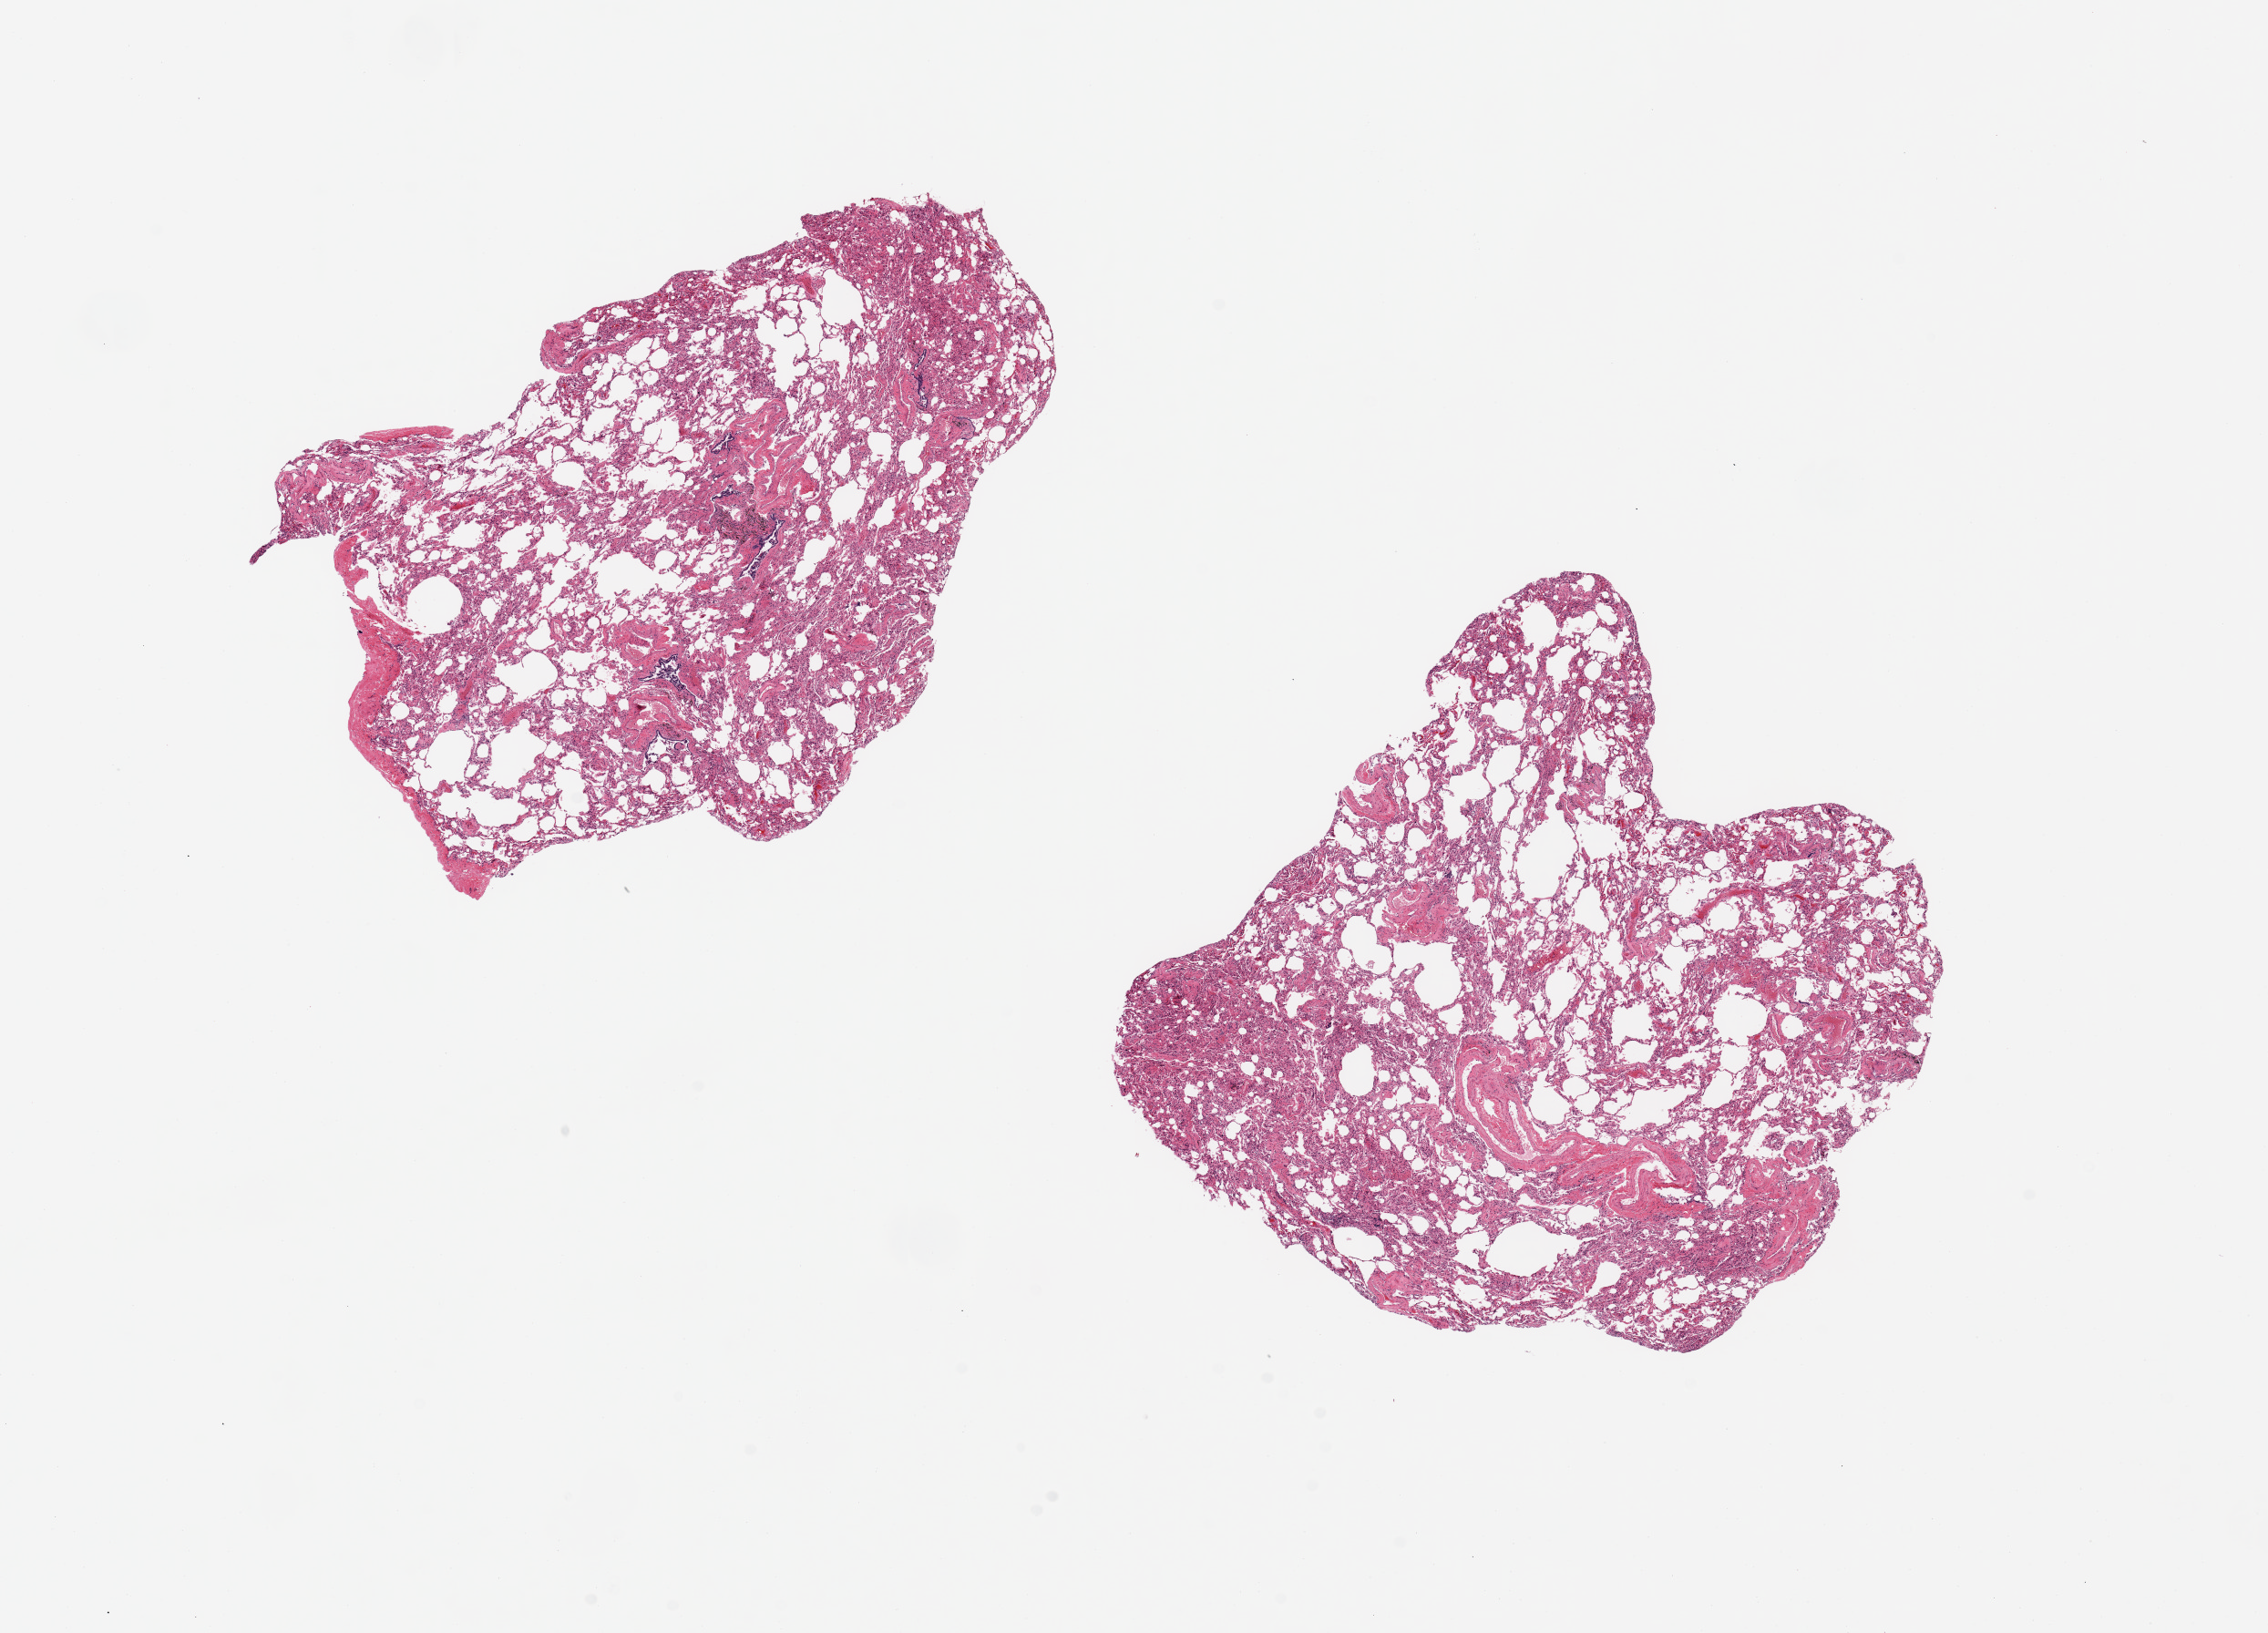
Whole-slide image, hematoxylin and eosin (H&E) stain, brightfield — a low-resolution overview of the entire scanned area, about 19.7 x 14.2 mm (acquisition: 20x scan), PAXgene-fixed, paraffin-embedded tissue, target tissue: lung, donor tissue sample. Donor sex: male.
Reviewer comment on this tissue sample: 2 pieces, 7x5 & 6x6mm; focally atelectatic.